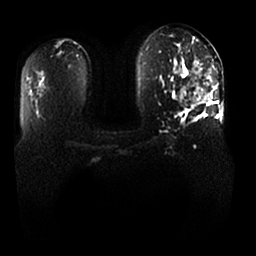
Breast MRI, one axial slice; slice 14 of 25 in the series (ordered by position); diffusion-weighted series; image 2 of 4 stored at this slice position (different b-values; order by instance number); 1.5 T; 4 mm slice thickness; 256 × 256 image matrix, field of view 370 × 370 mm. Female patient.
Outlined on this slice (outlined manually by an expert reader):
- tumour on diffusion-weighted imaging: bounding box <178,86,218,104> (left, top, right, bottom; pixels)